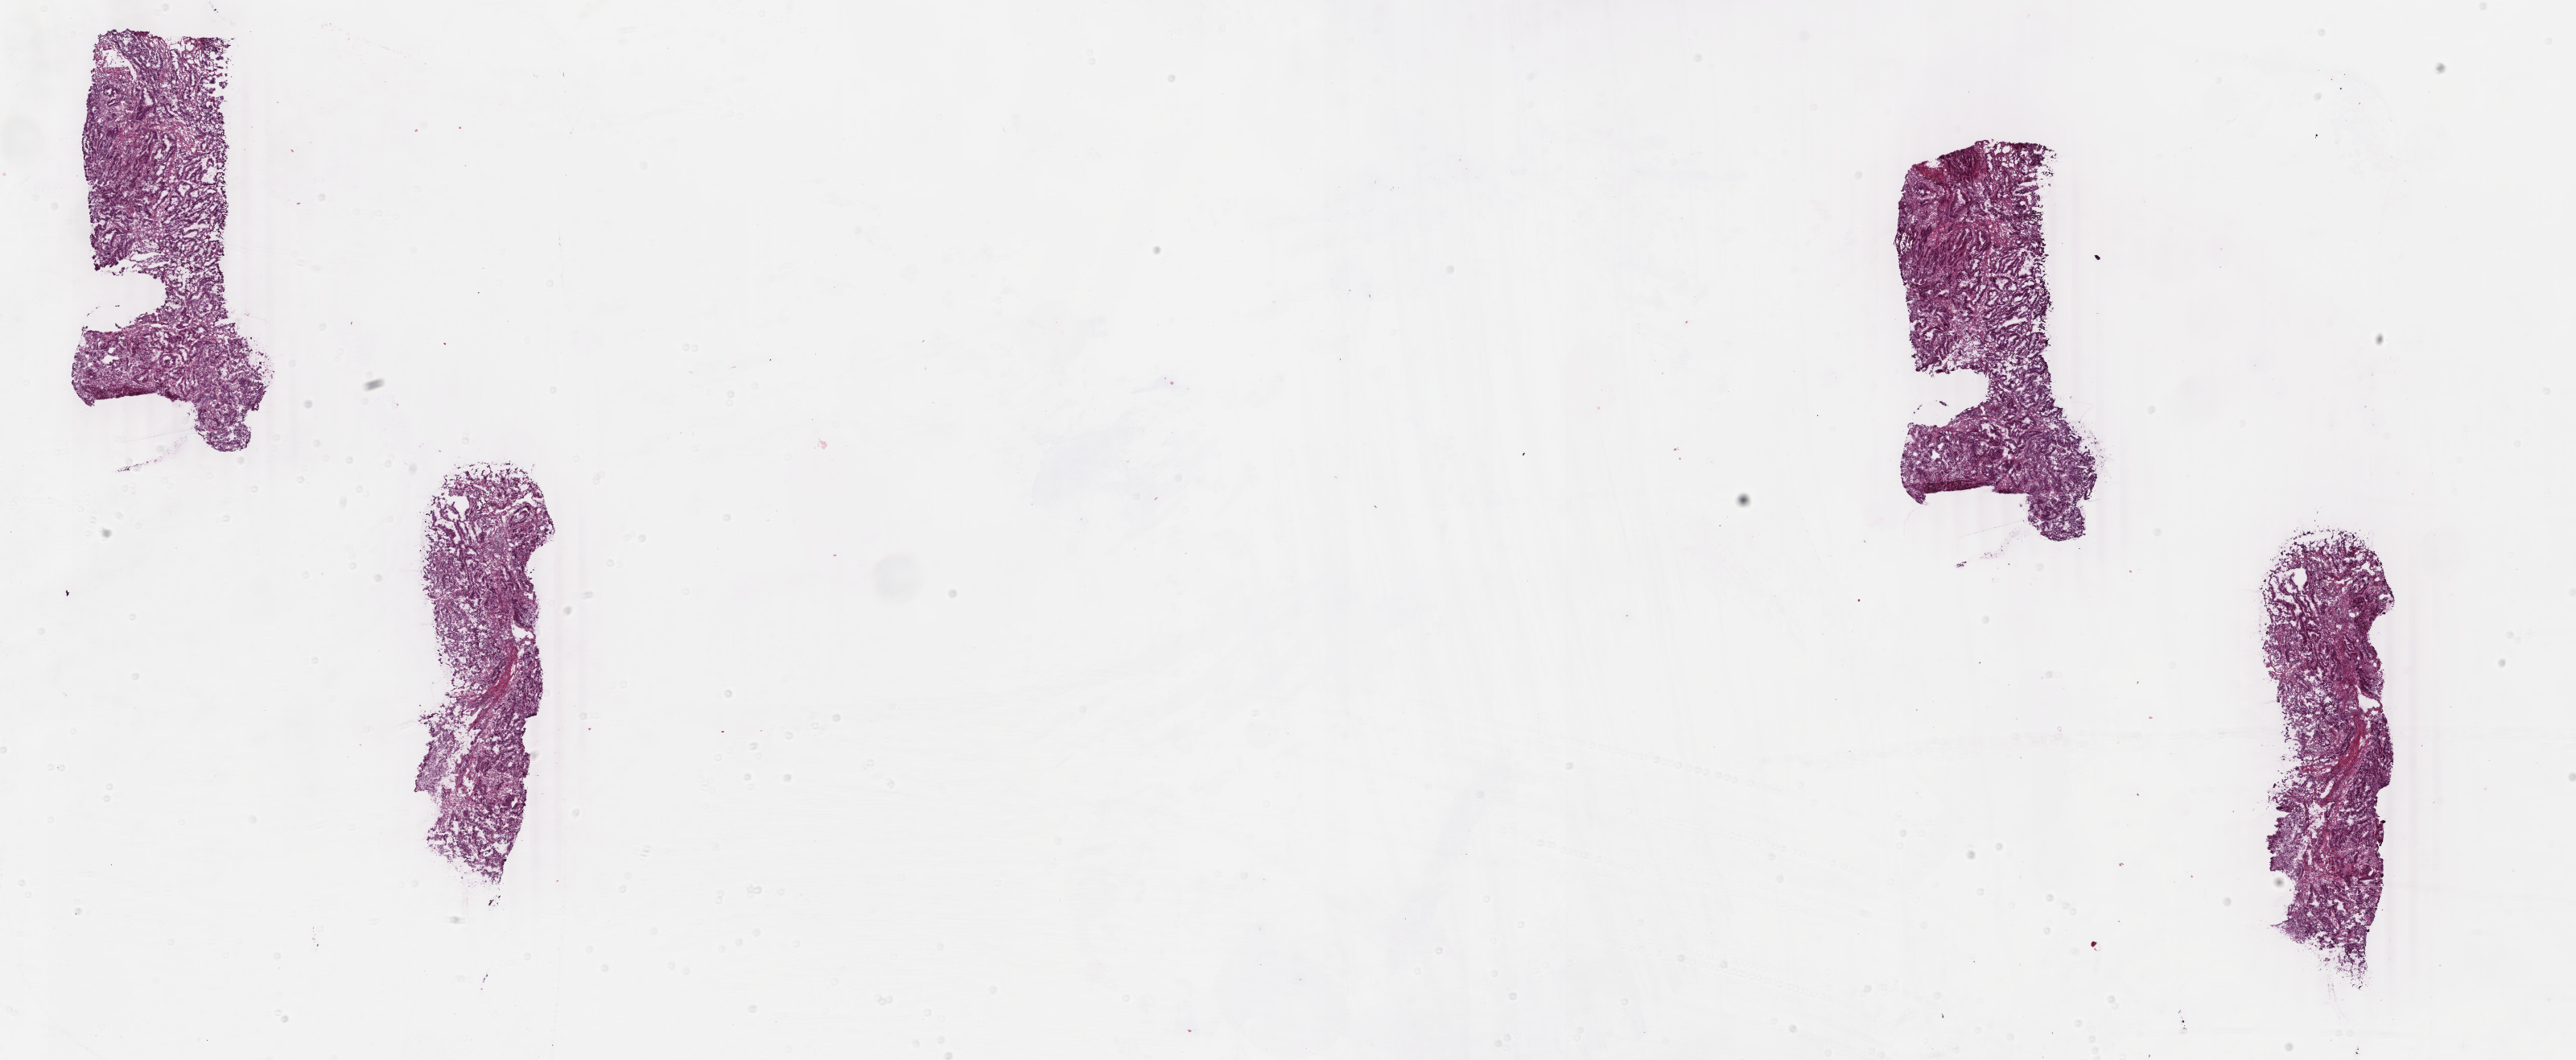
Whole-slide histology image, H&E, whole scanned area (about 25.5 x 10.5 mm) shown as a low-resolution overview; frozen section from the top of the tissue portion; primary tumour sample from the uterus. Female patient; age at initial diagnosis 63 years. Histologic grade: G1 (well differentiated). Composition of this section per pathologist review: tumour cells 65%, tumour nuclei 60%, normal cells 25%, stromal cells 2%, necrosis 8%. Inflammatory infiltration, as recorded: lymphocyte infiltration 12%, monocyte infiltration 0%, neutrophil infiltration 1%.
FIGO stage: IB. Pathologic diagnosis: Endometrioid adenocarcinoma, NOS (endometrium).